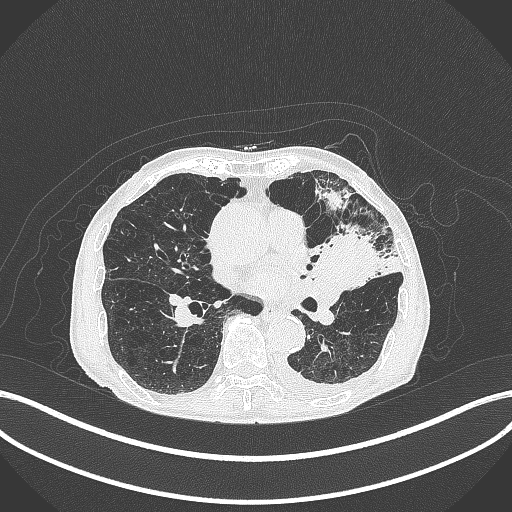
Chest CT, one axial slice; position 187 of 385 along the scan axis; reconstruction kernel B70f; 120 kVp; lung window (W 1500 / L -600 HU); 1 mm slice thickness; 512 × 512 image matrix. Male patient, age 90 years or older. From the clinical record (not read from this slice): clinical TNM (as recorded): T2b N1 M0.
Annotated regions visible in this slice (bounding box drawn by a radiologist):
- lung tumour (recorded histology: squamous cell carcinoma): bounding box [x1, y1, x2, y2] px = [314, 234, 379, 291]